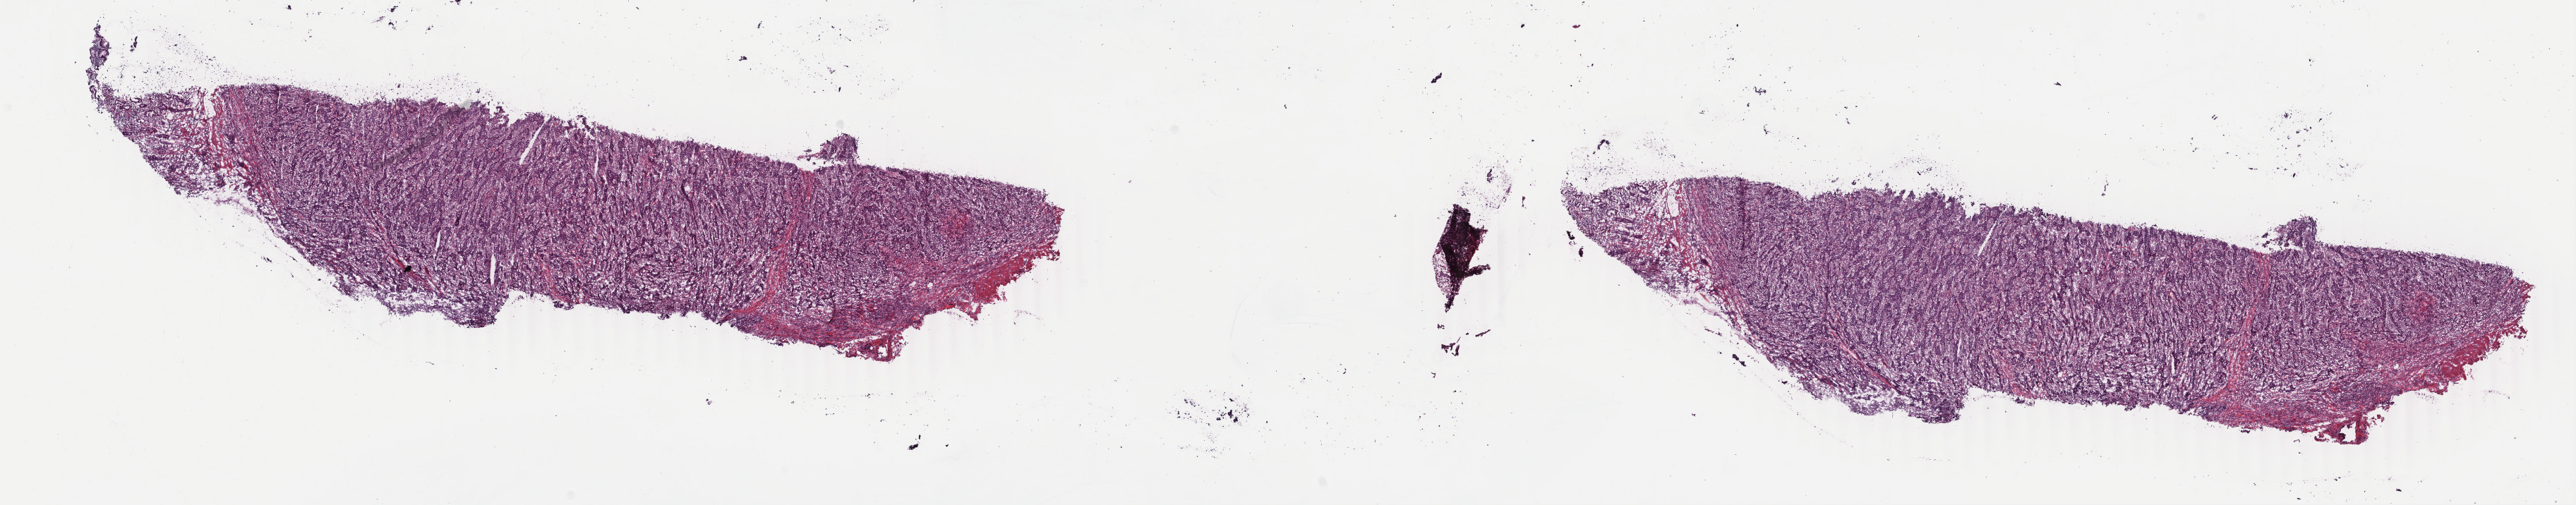
Whole-slide histology image, H&E-stained — low-resolution overview of the scanned area, about 29.0 x 5.7 mm; frozen section from the top of the tissue portion; primary tumour sample from the stomach. Male, age 72 years at initial diagnosis. Histologic grade: G3 (poorly differentiated). Slide review estimates, as recorded: tumour cells 50%, tumour nuclei 60%, normal cells 0%, stromal cells 50%, necrosis 0%. Infiltration values recorded for this section: lymphocyte infiltration 0%, monocyte infiltration 0%, neutrophil infiltration 100%.
Pathologic diagnosis: Adenocarcinoma, NOS (gastric antrum). TNM: T4a N2 M0. AJCC pathologic stage: IIIB. Lymph nodes positive (case pathology): 3 of 8 examined.